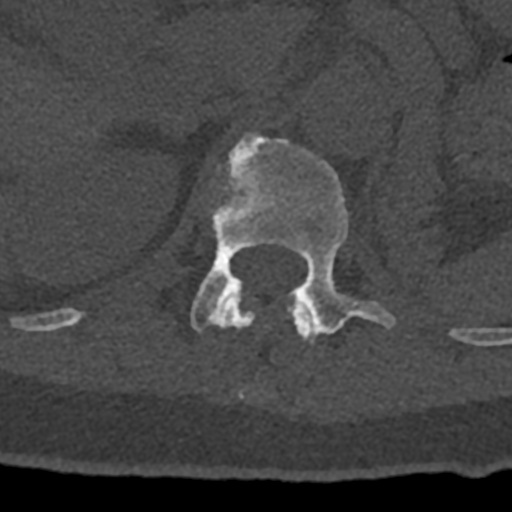
CT including the spine, one axial slice; slice 454 of 797 in the series (ordered by position); 120 kVp; bone window (W 1800 / L 400 HU); 0.5 mm slice thickness; 512 × 512 image matrix, field of view 160 × 160 mm. Male patient, age 74 years. Case-level facts recorded for this patient, not image findings: primary cancer: renal; vertebrae with lytic lesions (as recorded): T10, L1, L2, L3, L4, L5.
Annotated regions visible in this slice (semi-automatic segmentation, software-assisted and operator-edited):
- L1 vertebra: bounding box <191,132,396,337> (left, top, right, bottom; pixels)
- T12 vertebra: <70,299,314,343>